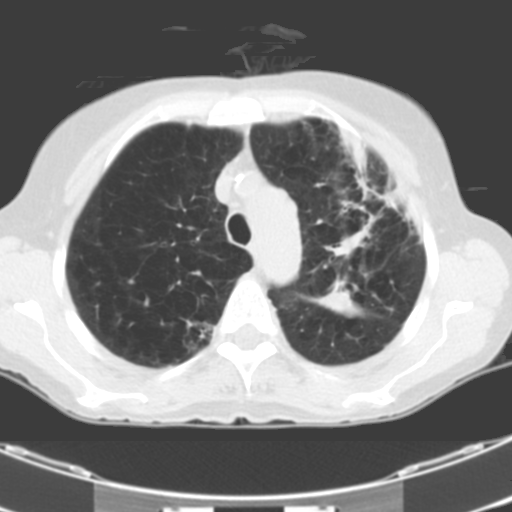
Low-dose screening chest CT, one axial slice. Position 81 of 106 along the scan axis. 120 kVp. One of 2 acquisitions stored at this slice position. Lung window (W 1500 / L -600 HU). 3.2 mm slice thickness. 512 × 512 image matrix, field of view 299 × 299 mm.
Outlined on this slice (outlined manually by an expert reader):
- lesion 1 (tumor): box from (x=318, y=289) to (x=358, y=317) px